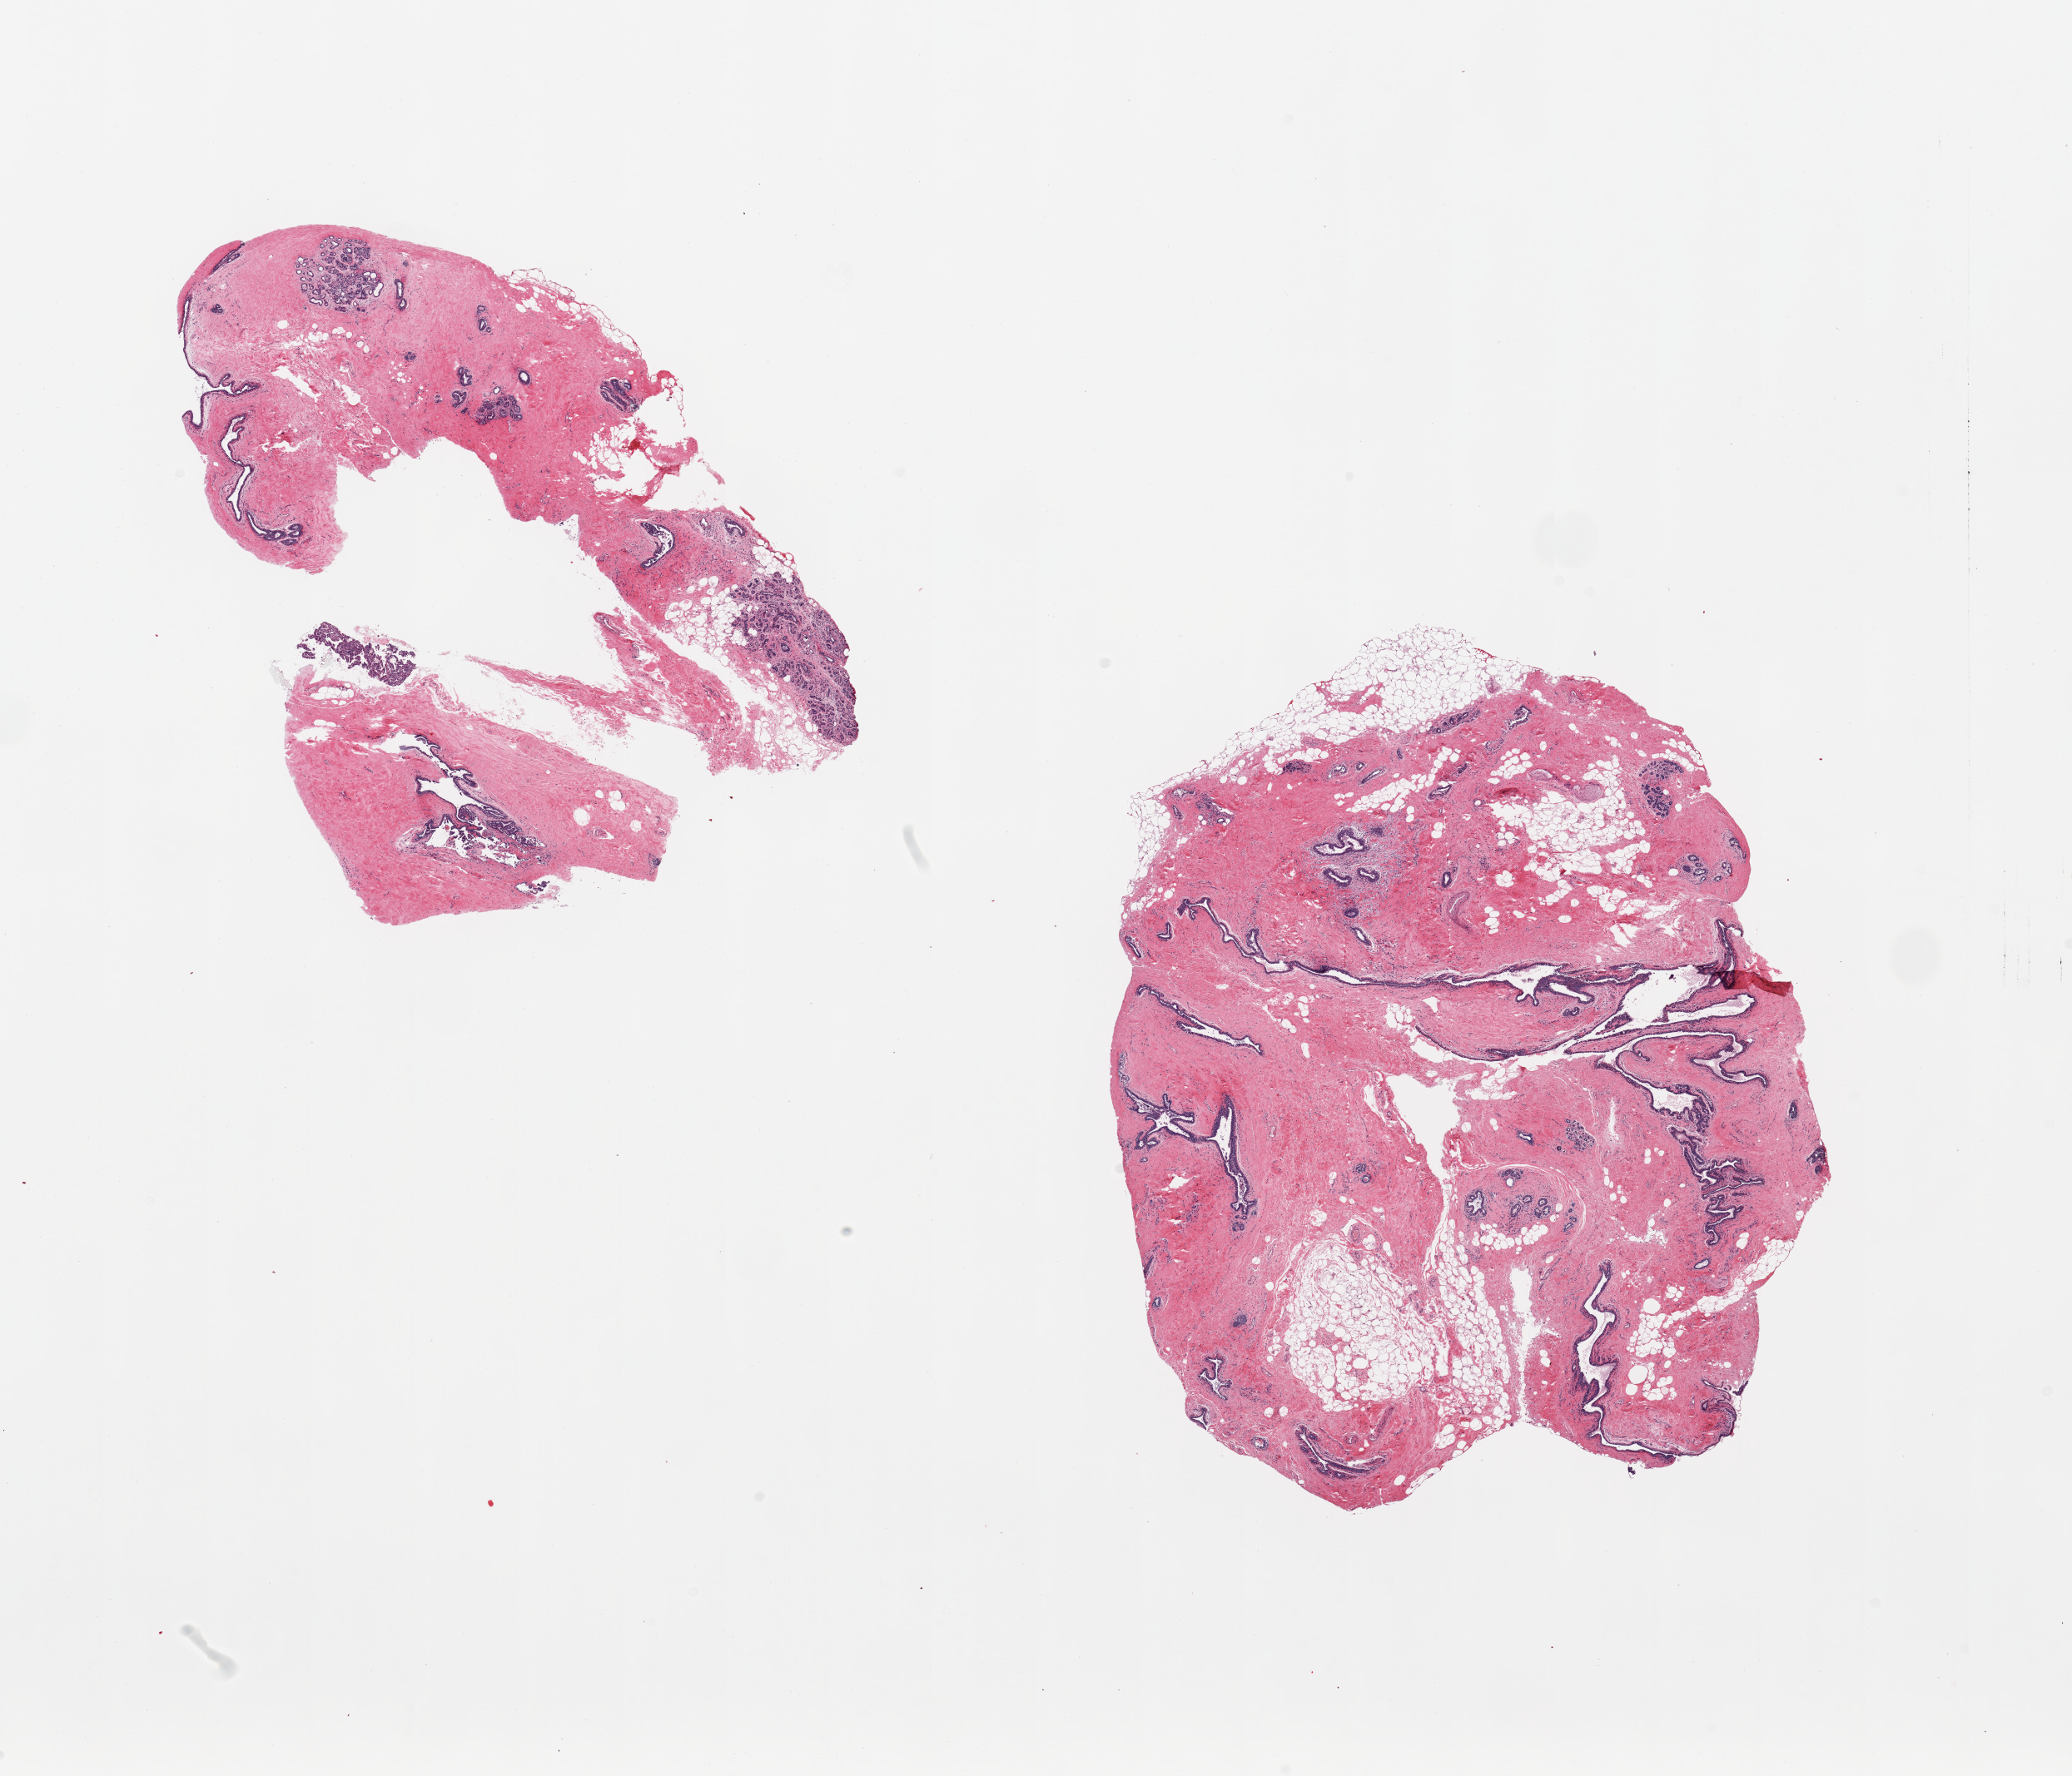
Hematoxylin and eosin (H&E) whole-slide image, whole scanned area (about 19.7 x 16.9 mm, acquisition: 20x scan) shown as a low-resolution overview, PAXgene-fixed paraffin-embedded (PFPE) section, sampled site (target tissue): breast, tissue donor sample. Donor: female.
• reviewer comment on this tissue sample: 2 pieces; predominantly stroma with some adipose tissue, ductal hyperplasia